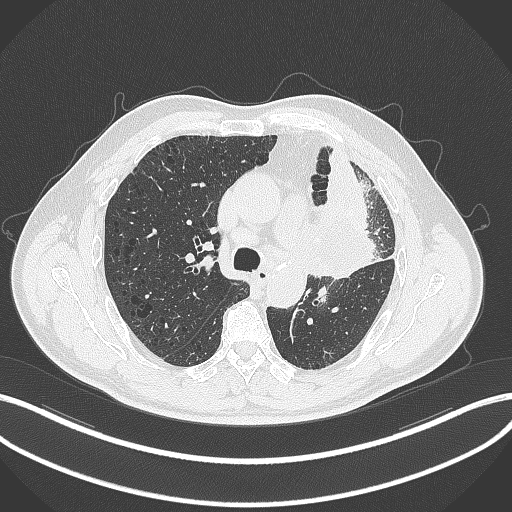
Chest CT, one axial slice; position 203 of 297 along the scan axis; 120 kVp; lung window (W 1500 / L -600 HU); 512 × 512 image matrix. Patient: male, 68 years. From the clinical record (not read from this slice): clinical TNM (as recorded): T3 N3 M1.
Outlined on this slice (rectangle marked by the reading radiologist):
- lung tumour (recorded histology: adenocarcinoma): box from (x=307, y=188) to (x=382, y=282) px